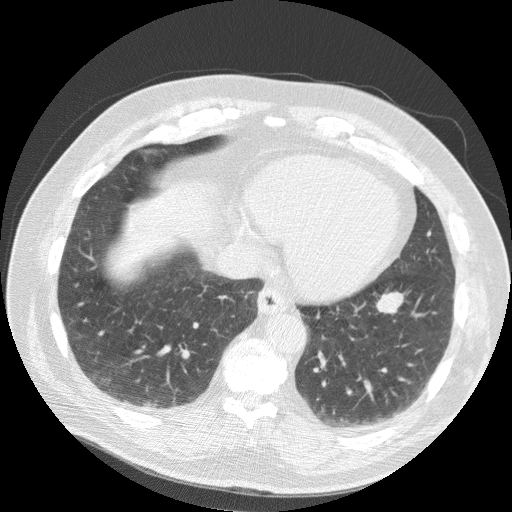
Chest CT (low-dose screening protocol), one axial image; second screening round (one year after baseline); lung window (W 1500 / L -600 HU); 120 kVp; 512 × 512 image matrix. Male, age 63 years at enrolment. Current smoker at enrolment.
Expert reader's lesion annotation, bounding box <362,285,410,324> (left, top, right, bottom; pixels). The screening reader recorded 2 non-calcified nodules or masses ≥4 mm on this exam (right middle lobe, left lower lobe); which of them this box marks is not recorded. Later outcome: lung cancer diagnosed 633 days after this screen — squamous cell carcinoma, NOS, left lower lobe, stage IB (AJCC 6th edition), 48 mm at pathology.